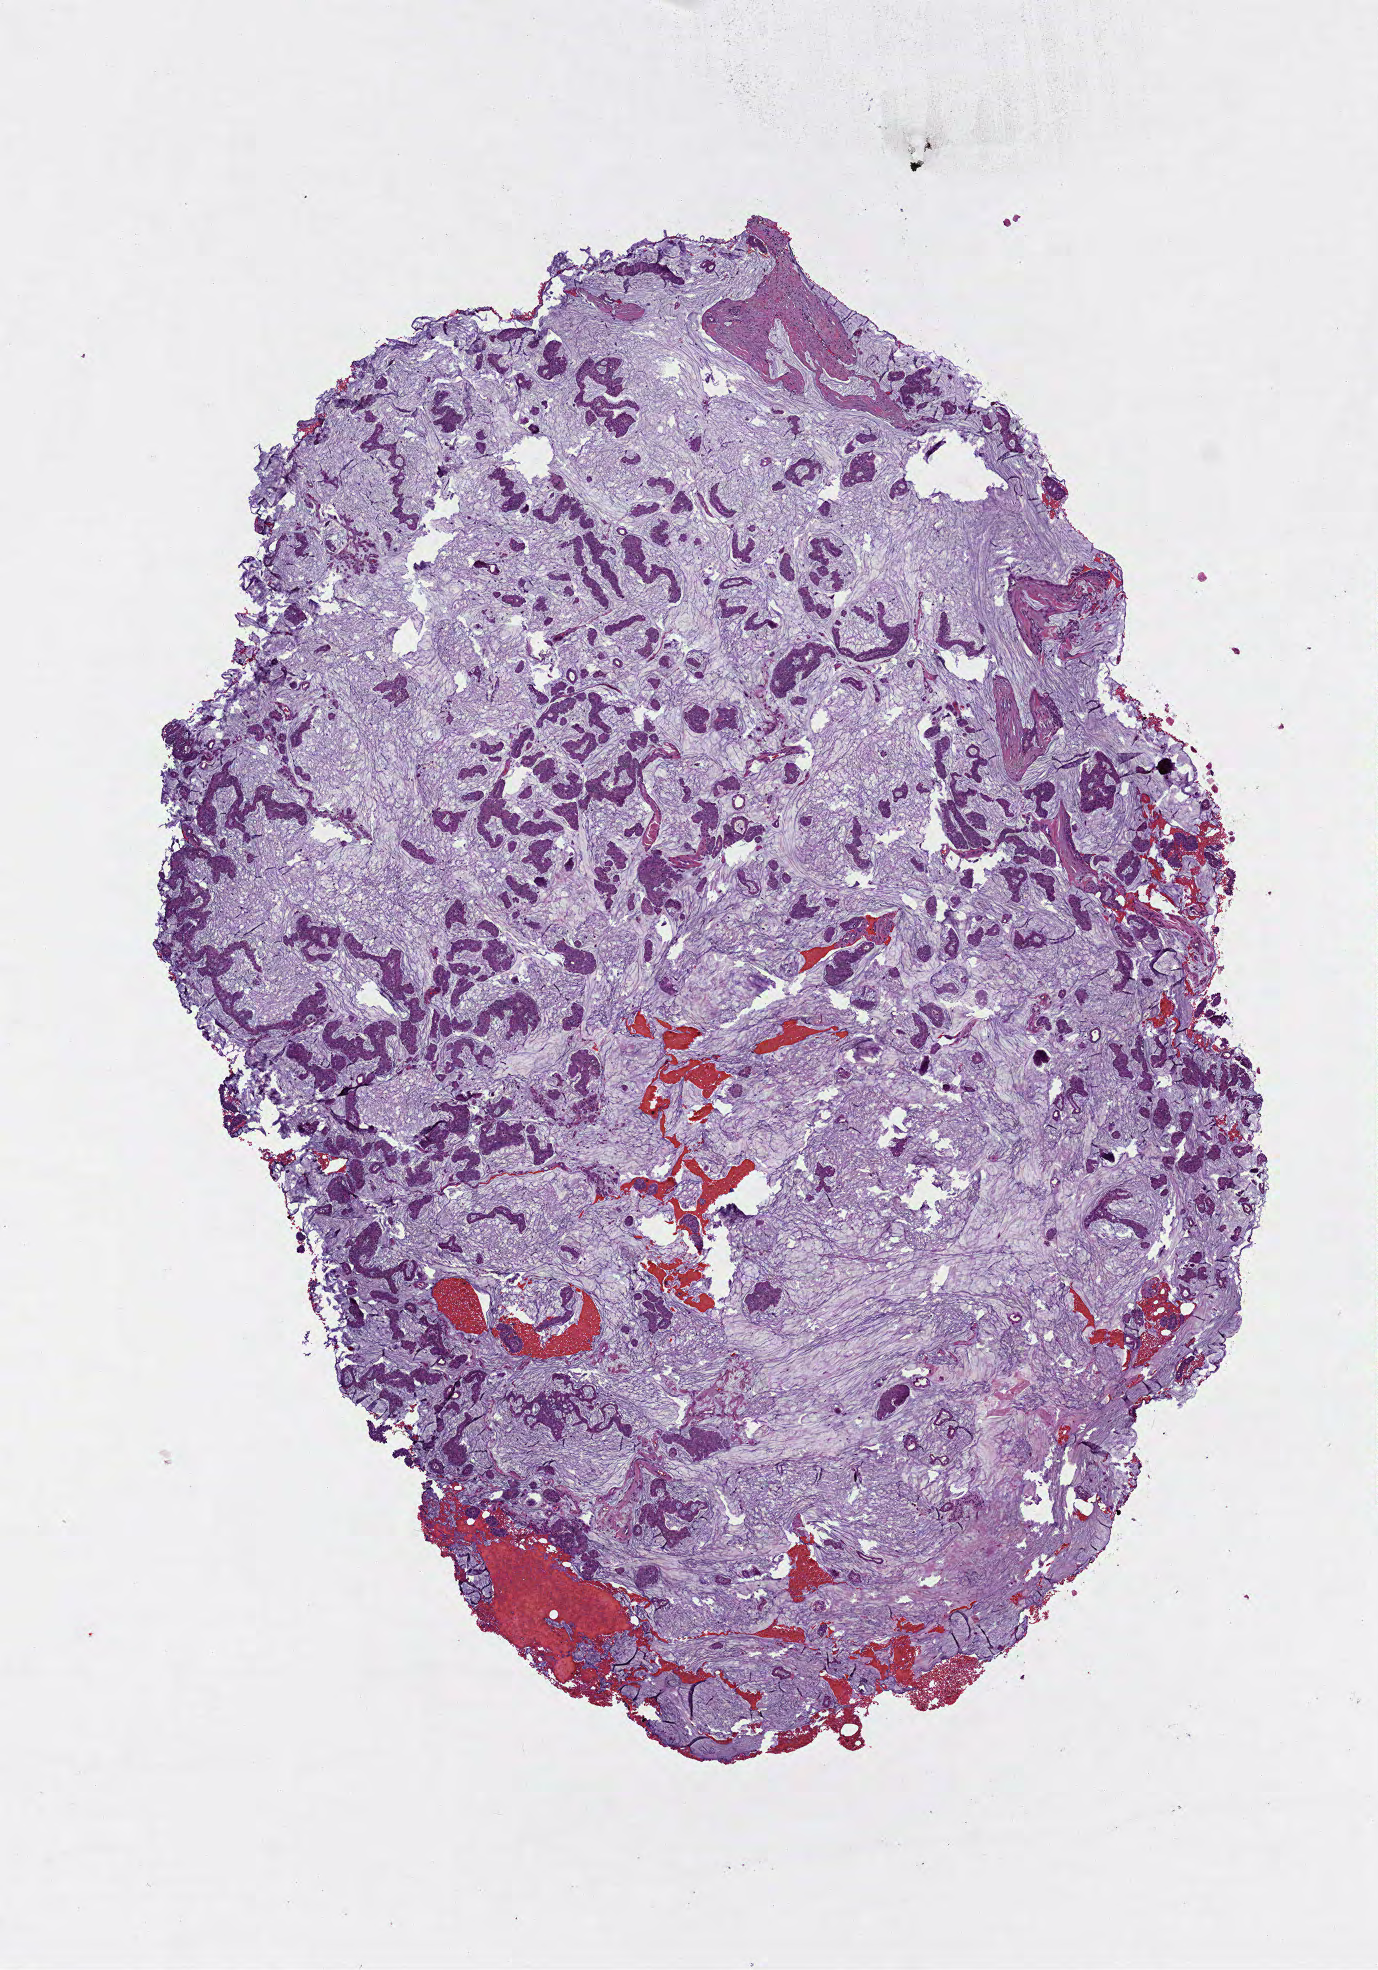
Hematoxylin and eosin (H&E) stained whole-slide image, a low-resolution overview of the entire scanned area, about 5.6 x 7.9 mm (from a 40x scan); formalin-fixed paraffin-embedded (FFPE) diagnostic section; sample: primary tumour, breast. Patient: female, age at initial diagnosis 75 years.
Pathologic diagnosis: Mucinous adenocarcinoma. AJCC pathologic stage: IA. Lymph nodes positive (case pathology): 0 of 2 examined.